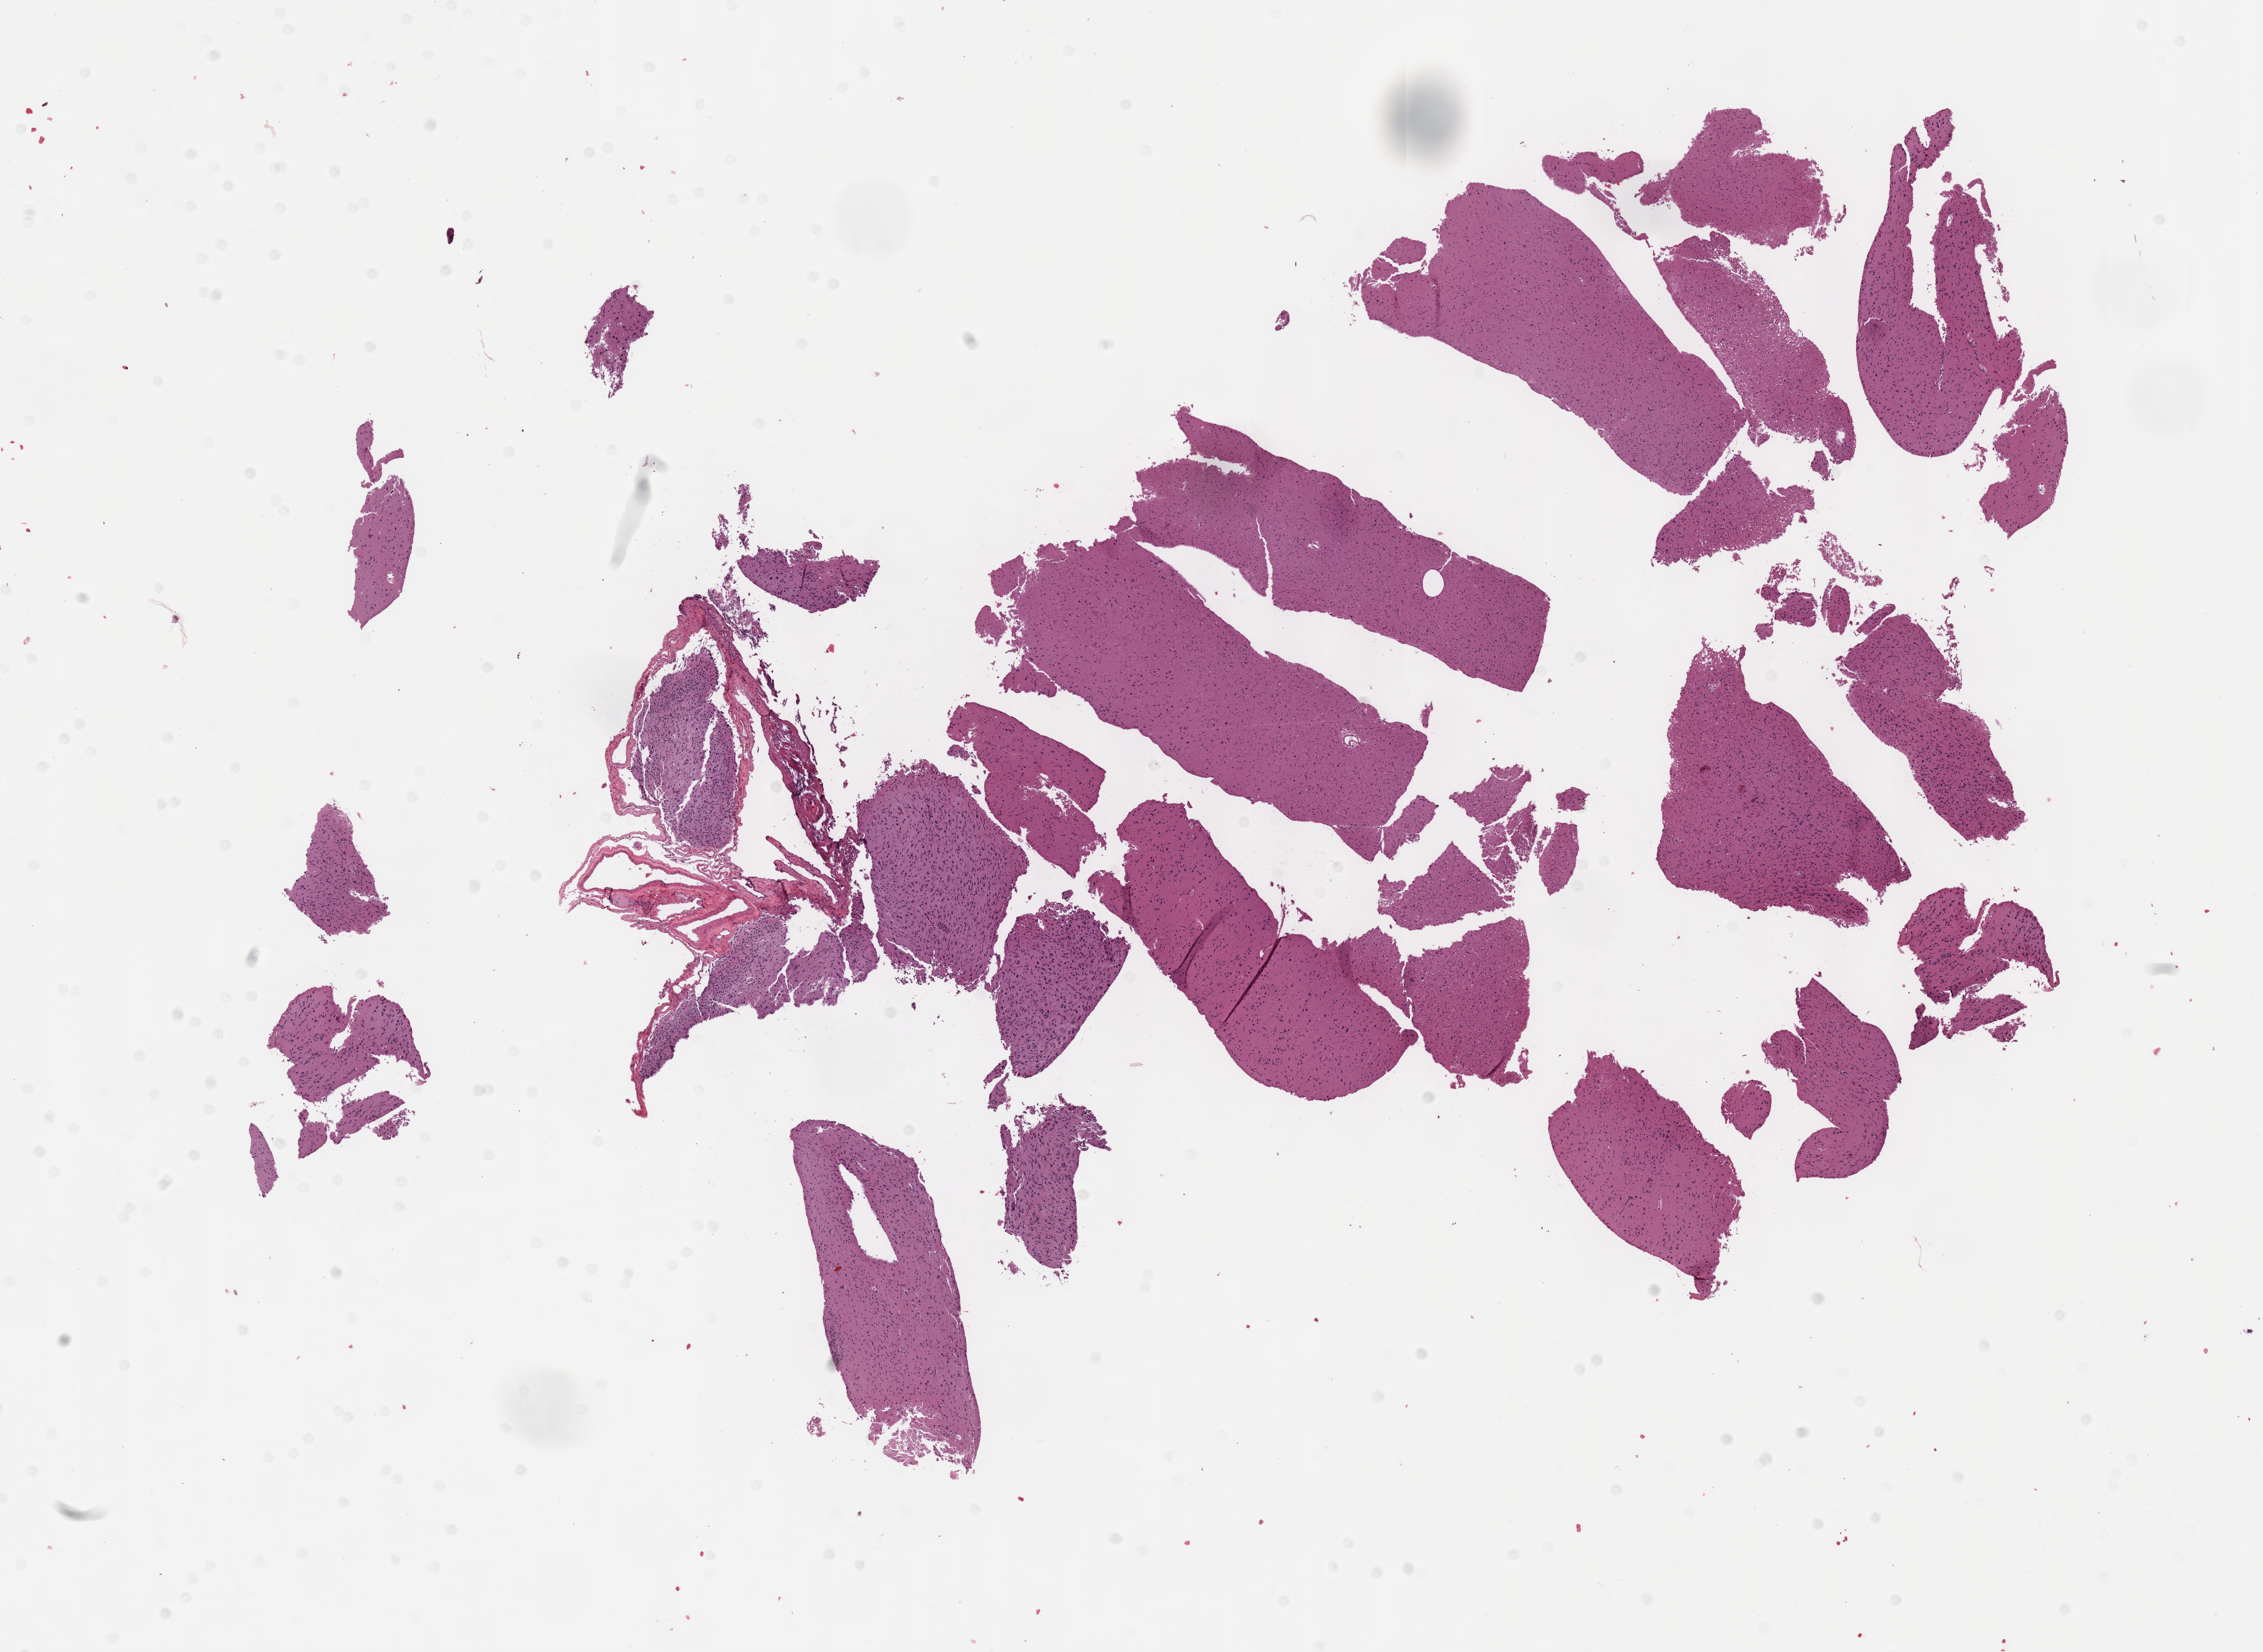
H&E whole-slide image — shown as a low-resolution overview of the whole scanned area (about 14.6 x 10.7 mm, from a 40x scan). Formalin-fixed paraffin-embedded (FFPE) diagnostic section. Sample: primary tumour, brain. Male patient; age at initial diagnosis 54 years. Histologic grade: G2 (moderately differentiated).
Diagnosis: Oligodendroglioma, NOS.